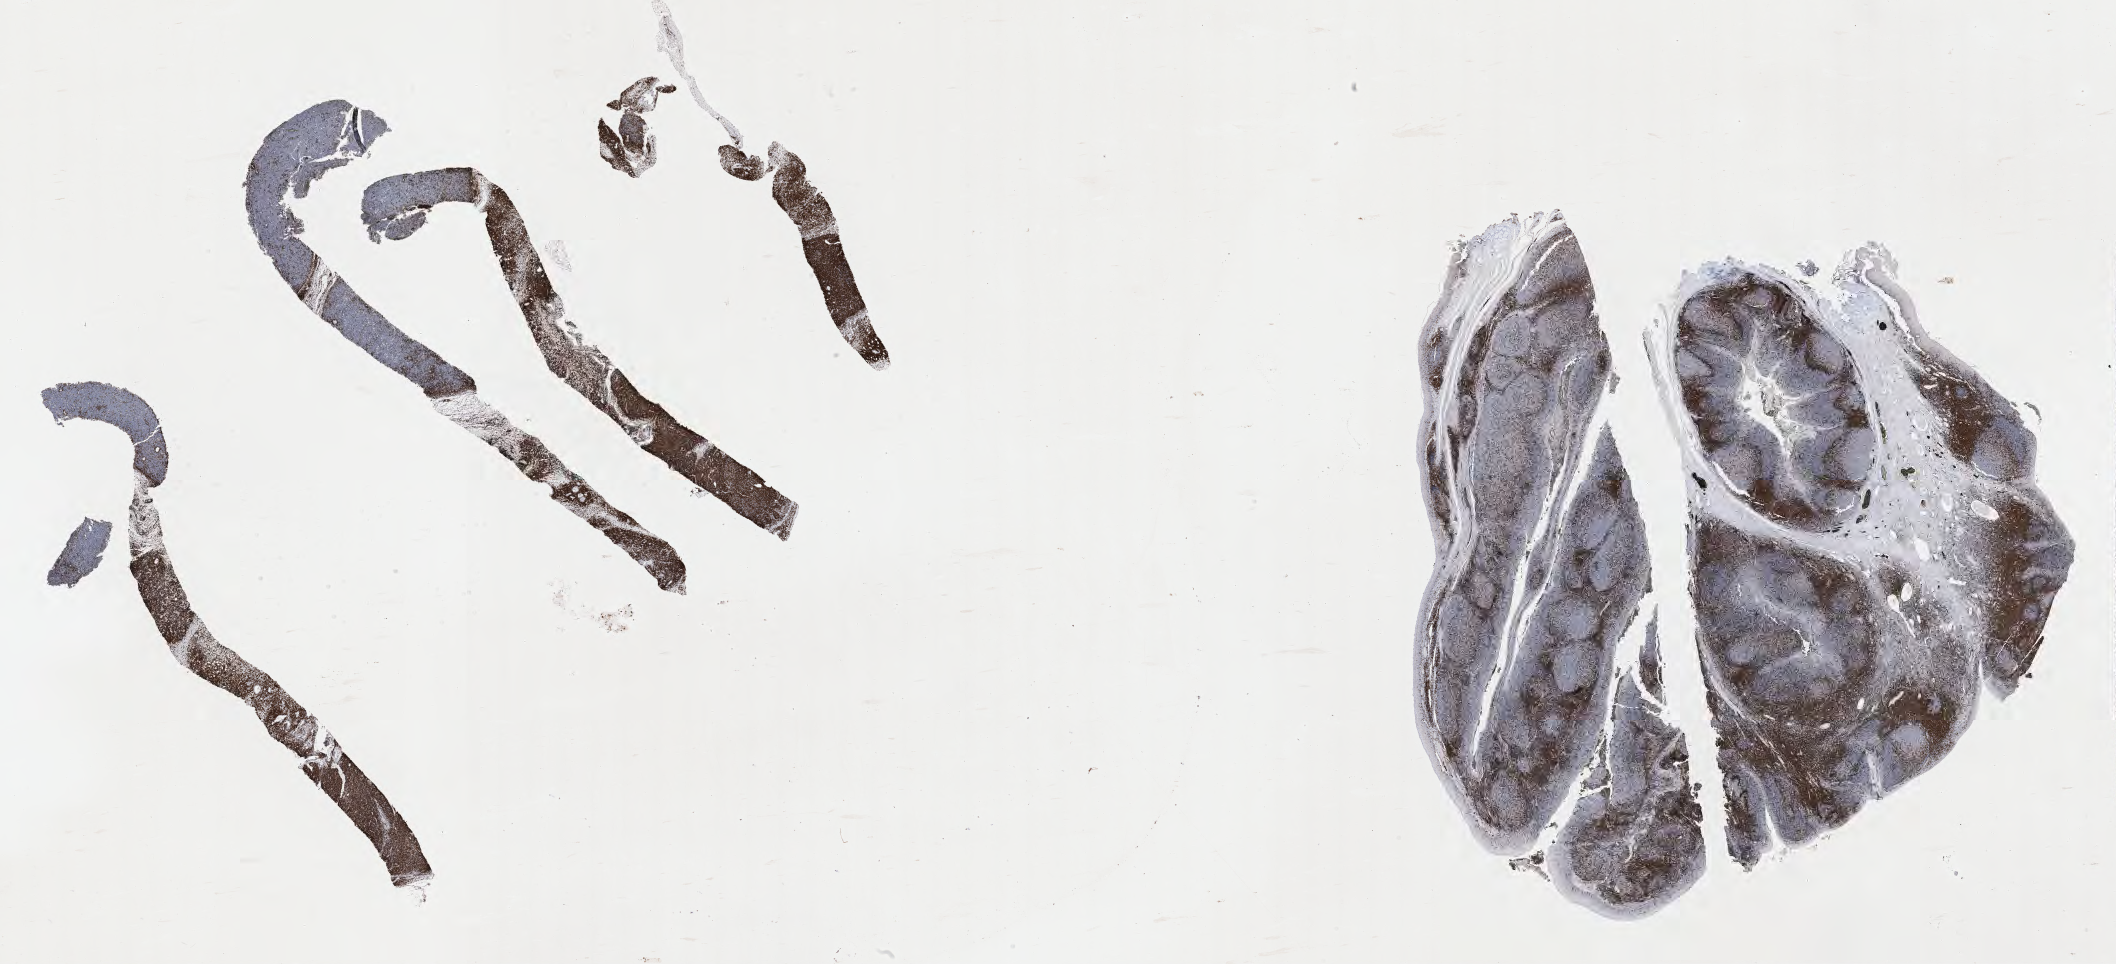
Whole-slide image, immunohistochemical stain for CD3, shown as a low-resolution overview of the whole scanned area (about 34.2 x 15.6 mm), tumor tissue. Patient male; 47 years old.
• diagnosis: Burkitt lymphoma, NOS